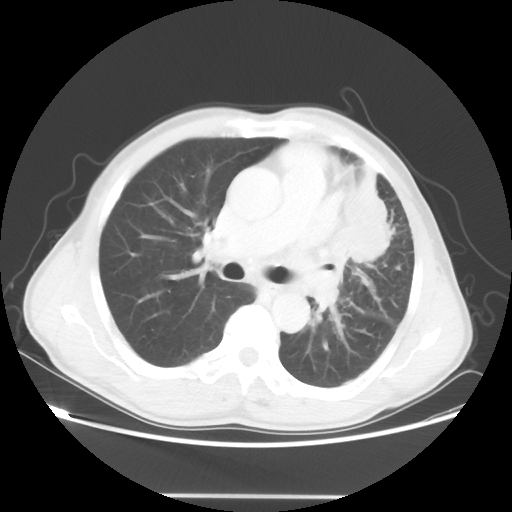
Chest CT, one axial slice. Slice 31 of 55 in the series (ordered by position). 100 kVp. Lung window (W 1500 / L -600 HU). 512 × 512 image matrix. Patient: male, 60 years. Case-level facts recorded for this patient, not image findings: clinical TNM (as recorded): T3 N3 M0.
Annotated regions visible in this slice (rectangle marked by the reading radiologist):
- lung tumour (recorded histology: adenocarcinoma): bounding box [x1, y1, x2, y2] px = [345, 164, 390, 271]